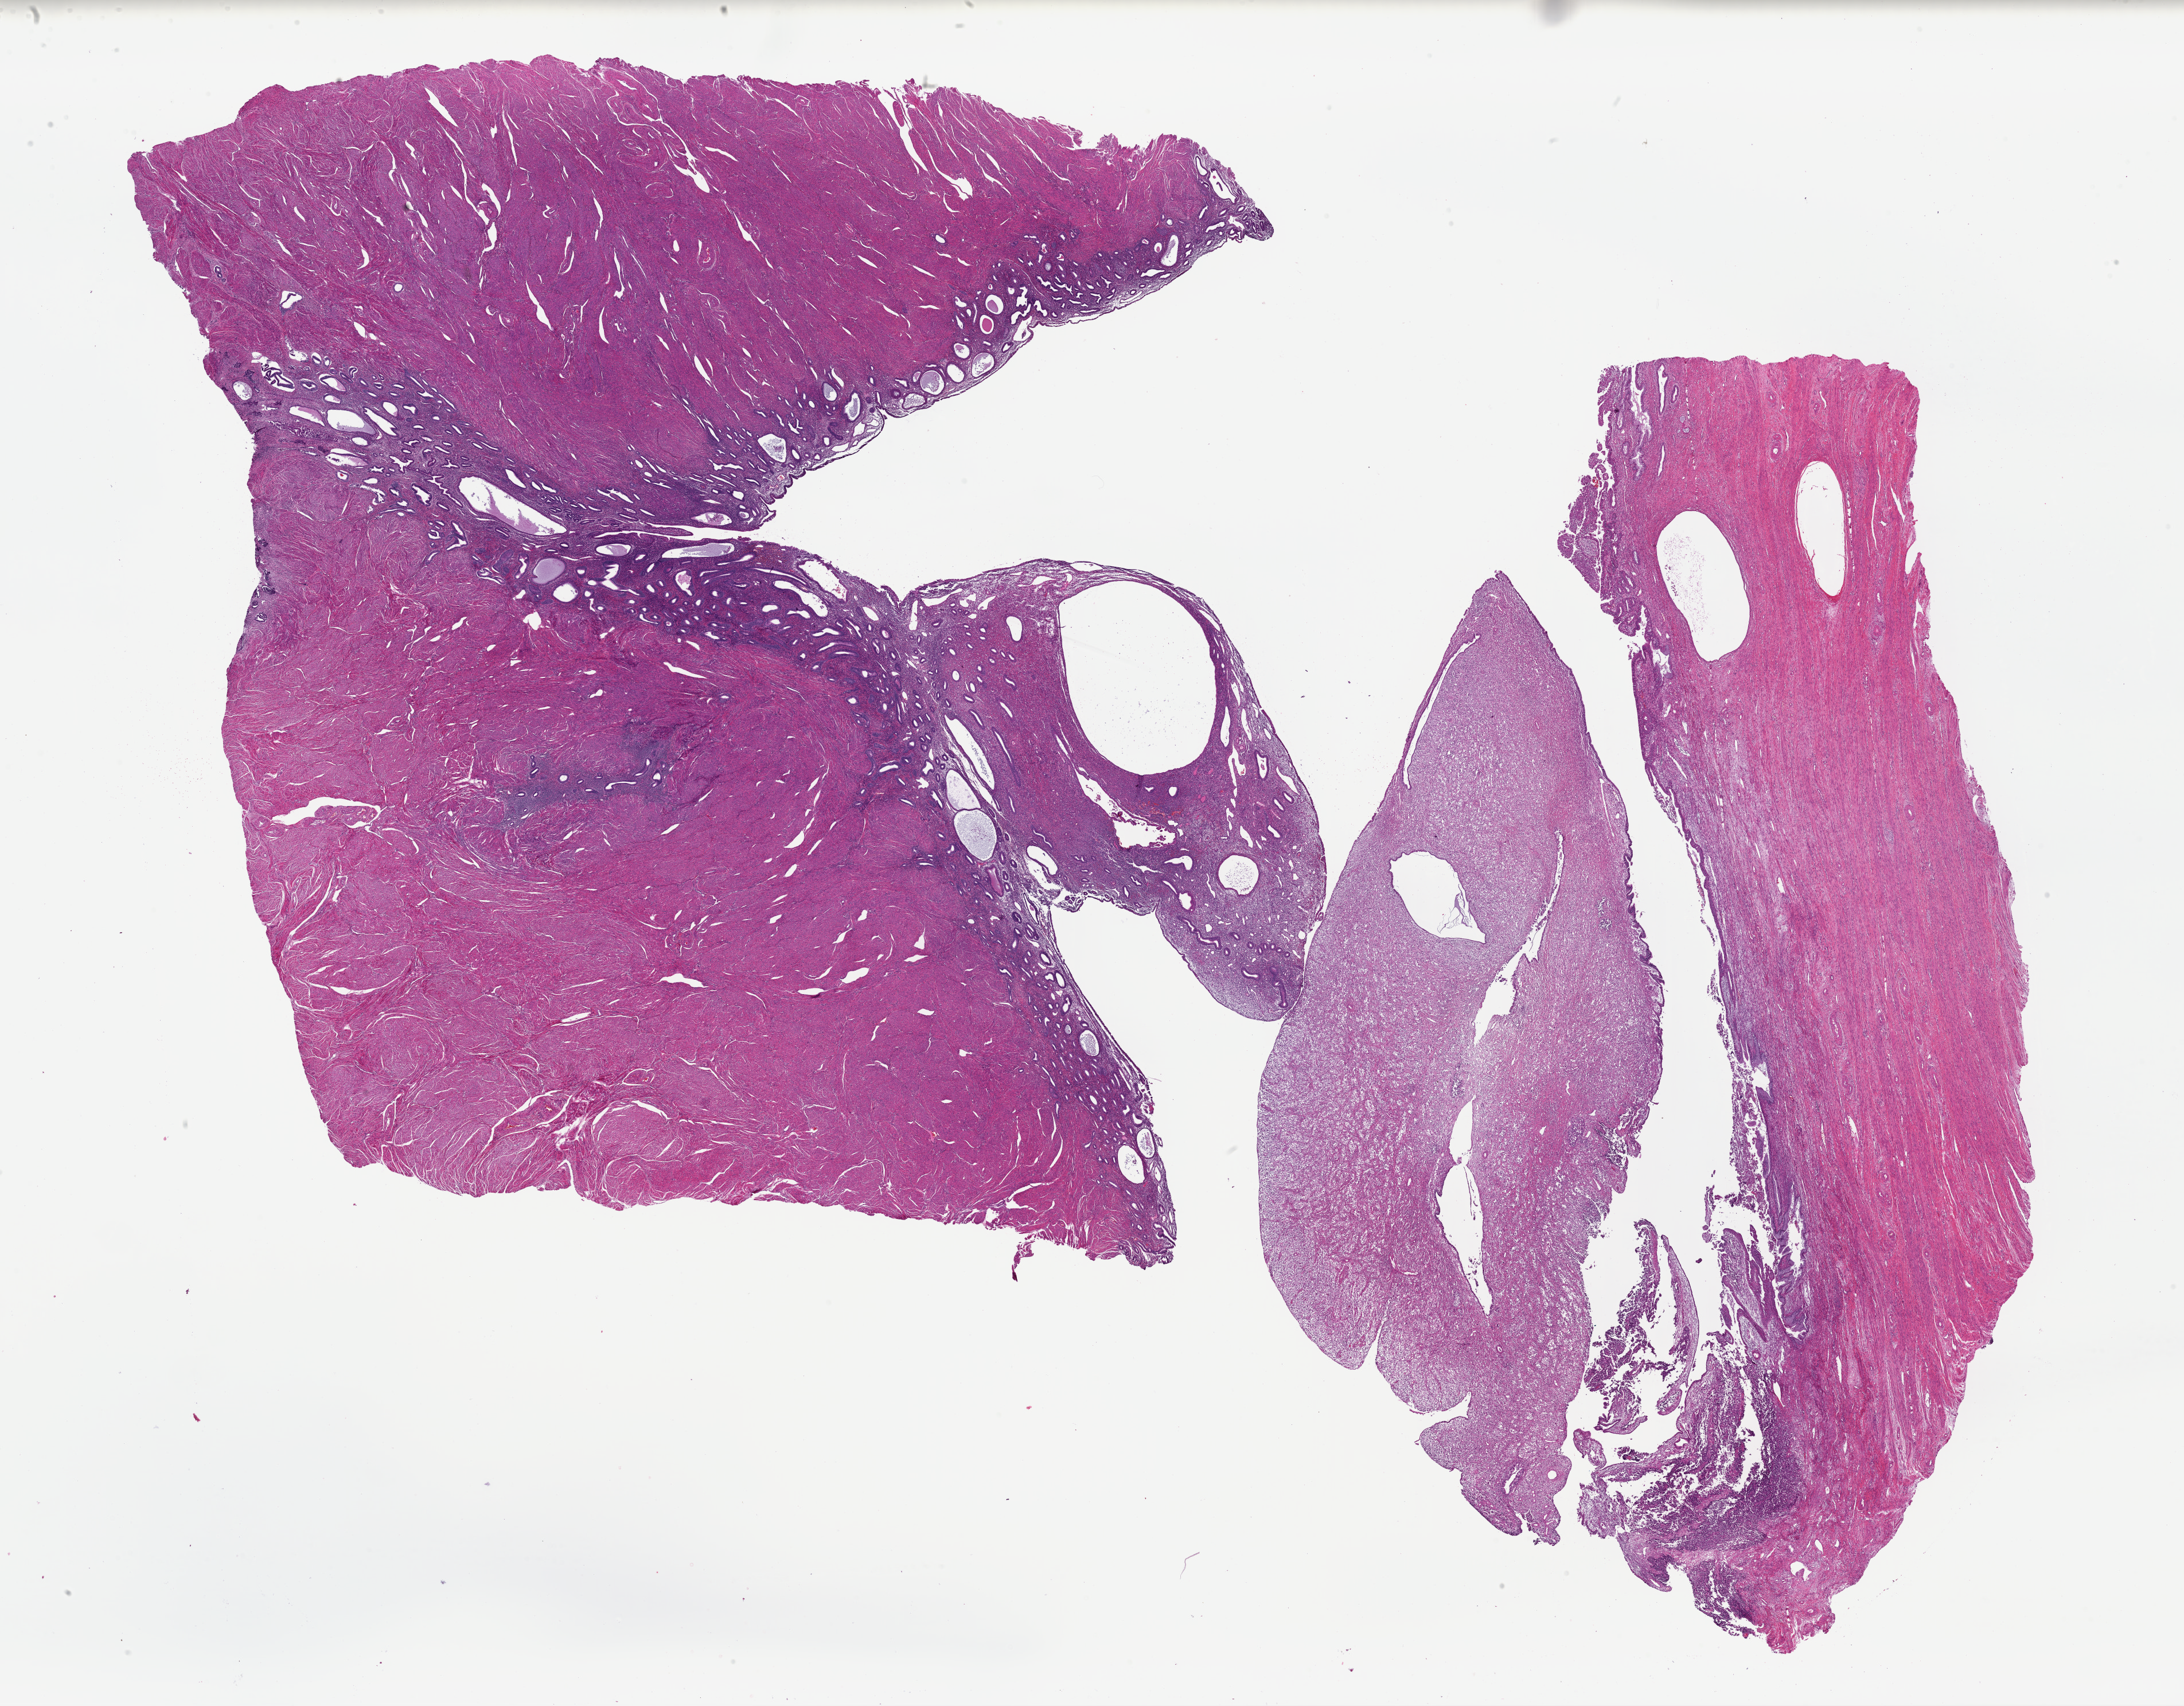
H&E whole-slide image, shown as a low-resolution overview of the whole scanned area (about 30.1 x 23.5 mm), formalin-fixed paraffin-embedded (FFPE) diagnostic section, sample: primary tumour, uterus. Female, age 60 years at initial diagnosis.
Diagnosis: Carcinosarcoma, NOS. FIGO stage: IVB.